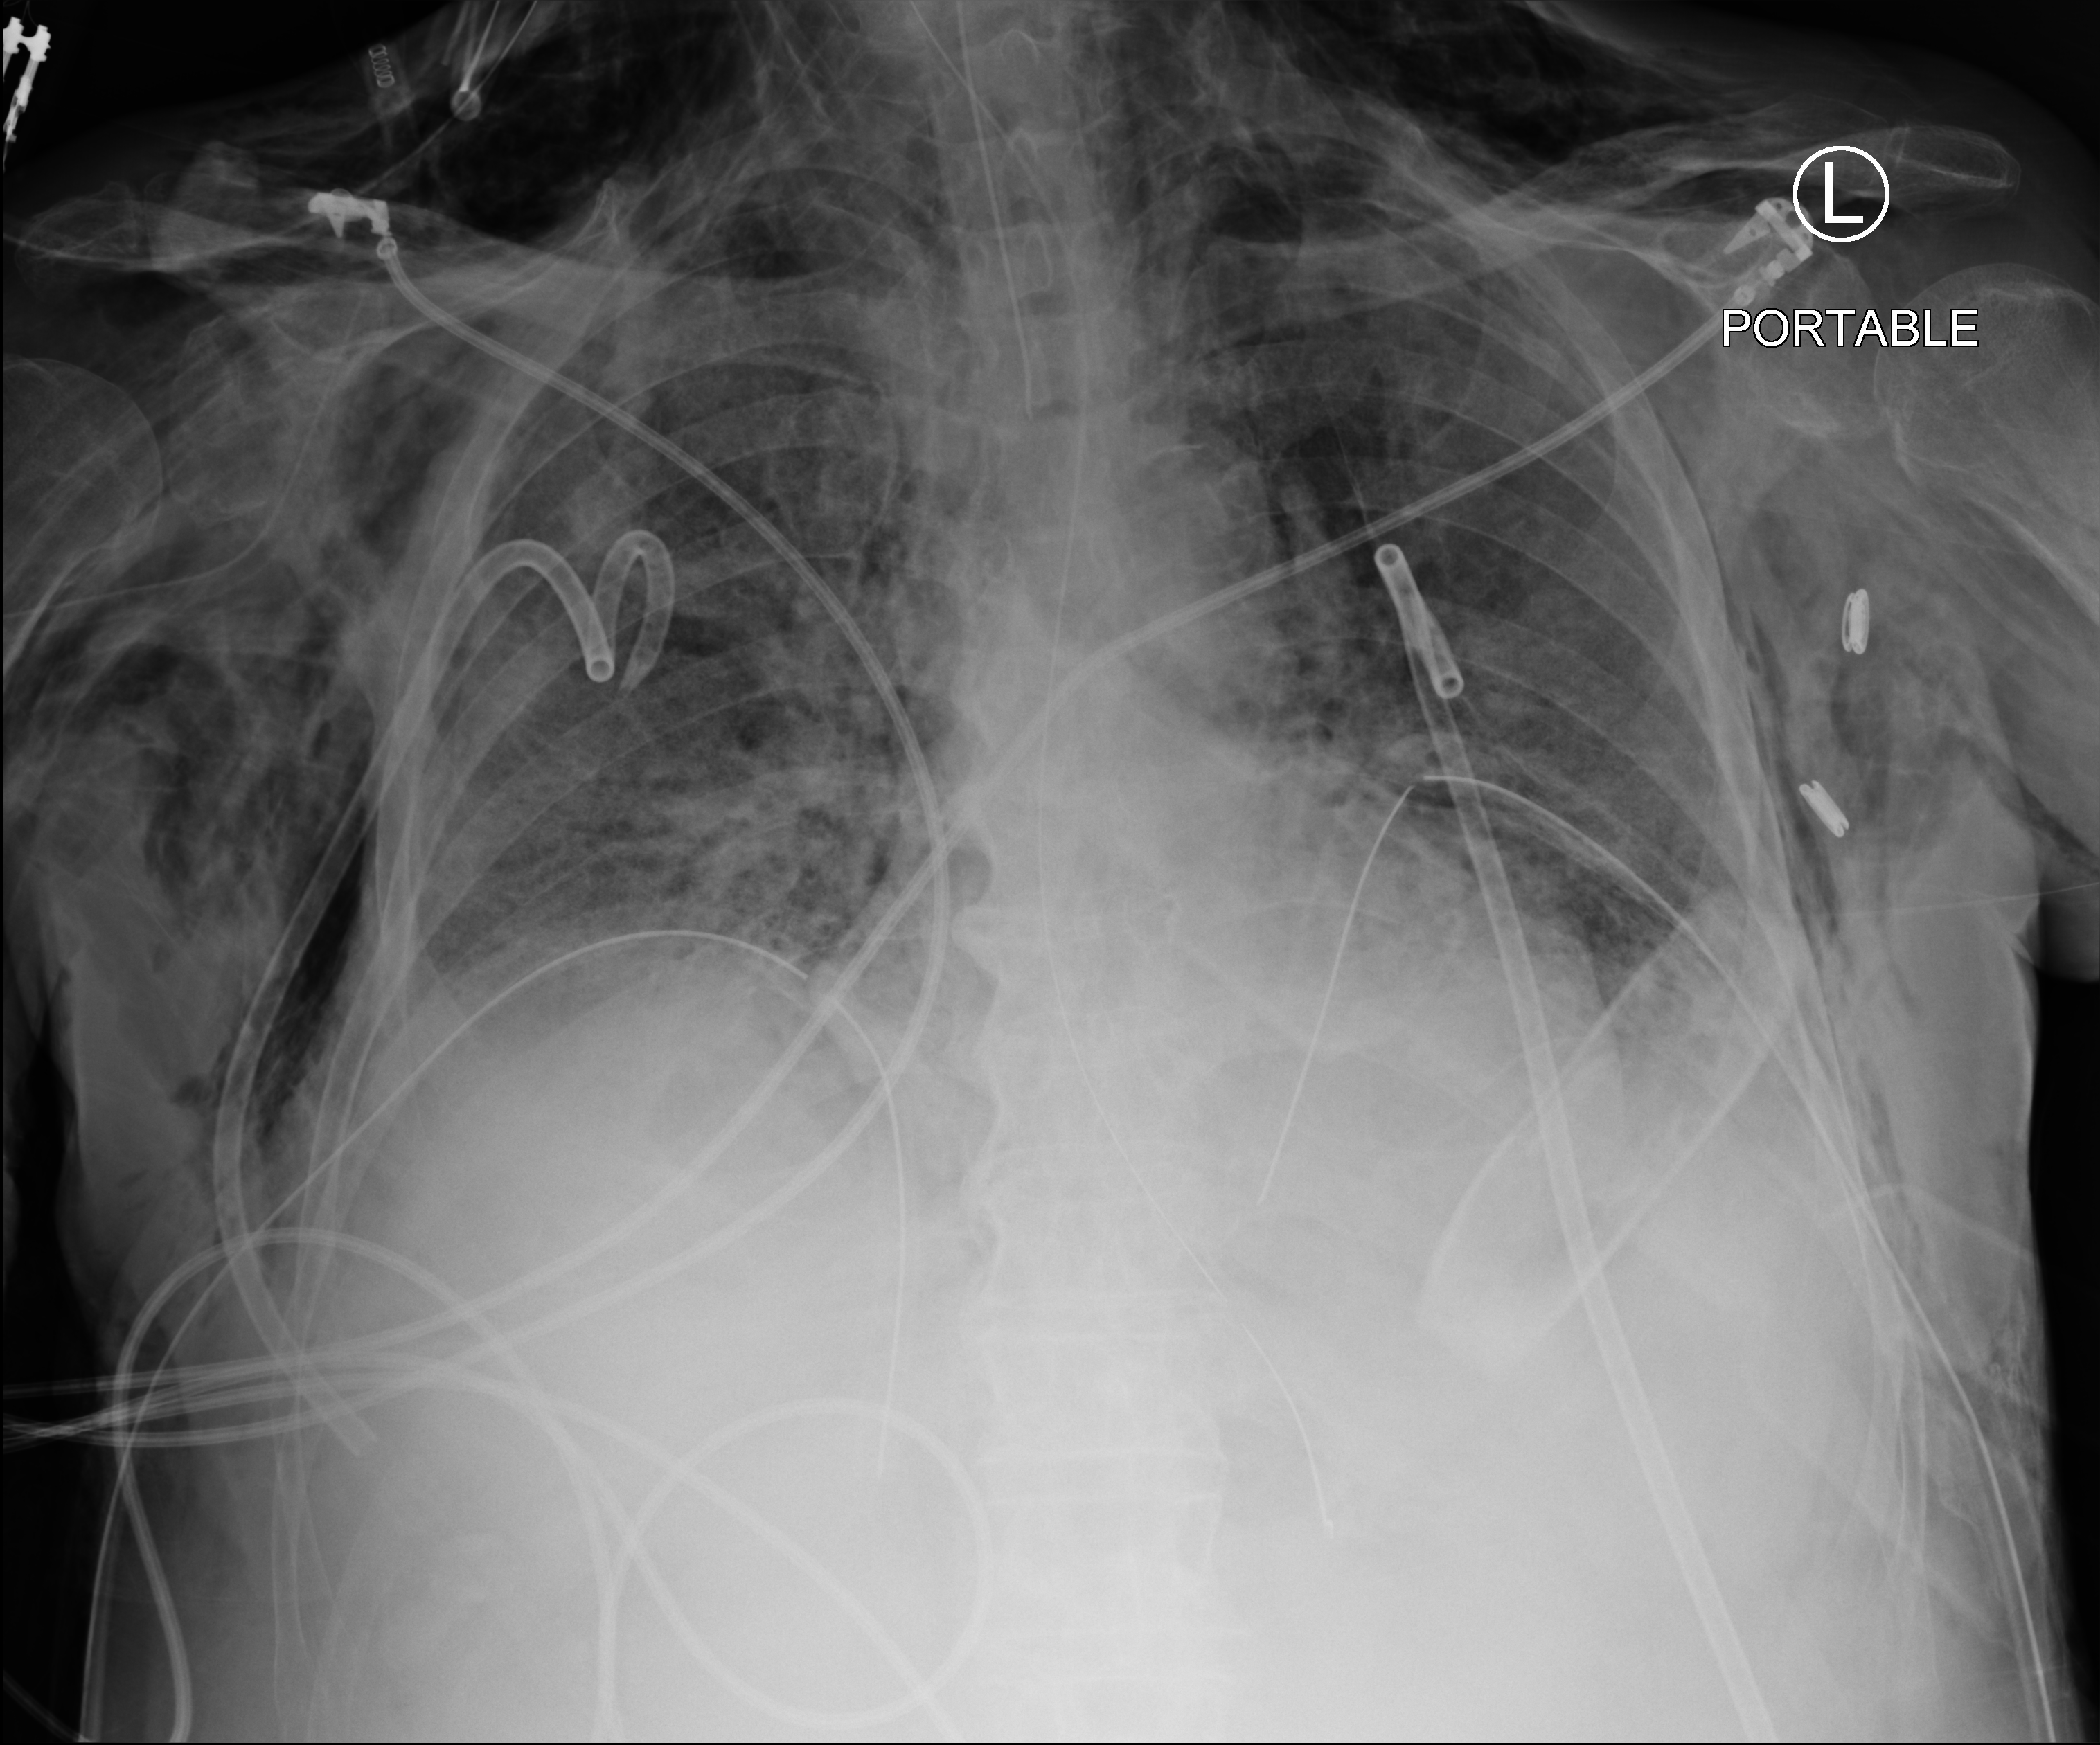
Portable chest radiograph; anteroposterior (AP) projection. Patient hospitalised with COVID-19; male, aged 75–90 years.
From the hospital-stay record, not from the radiograph (when in the stay this image was taken is not recorded):
- other chronic lung disease (admission record): no
- diabetes (admission record): no
- mechanically ventilated during this hospital stay: yes